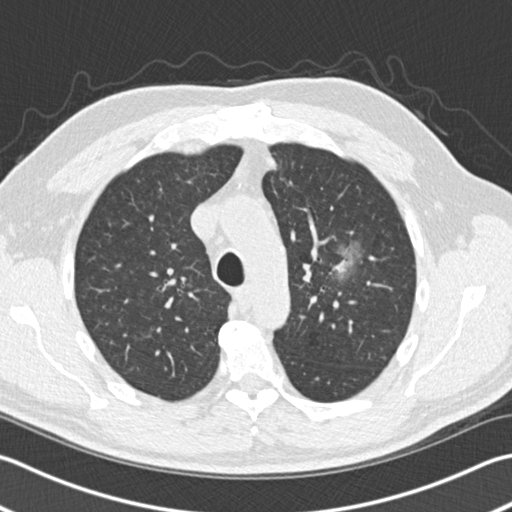
Low-dose screening chest CT, one axial slice. Slice 113 of 153 in the series (ordered by position). Lung window (W 1500 / L -600 HU). 2 mm slice thickness. 512 × 512 image matrix, field of view 346 × 346 mm.
Annotated regions visible in this slice (manually delineated by an expert):
- lesion 1 (tumor, upper lobe of left lung): bounding box (x1, y1, x2, y2) in pixels: (336, 261, 347, 273)